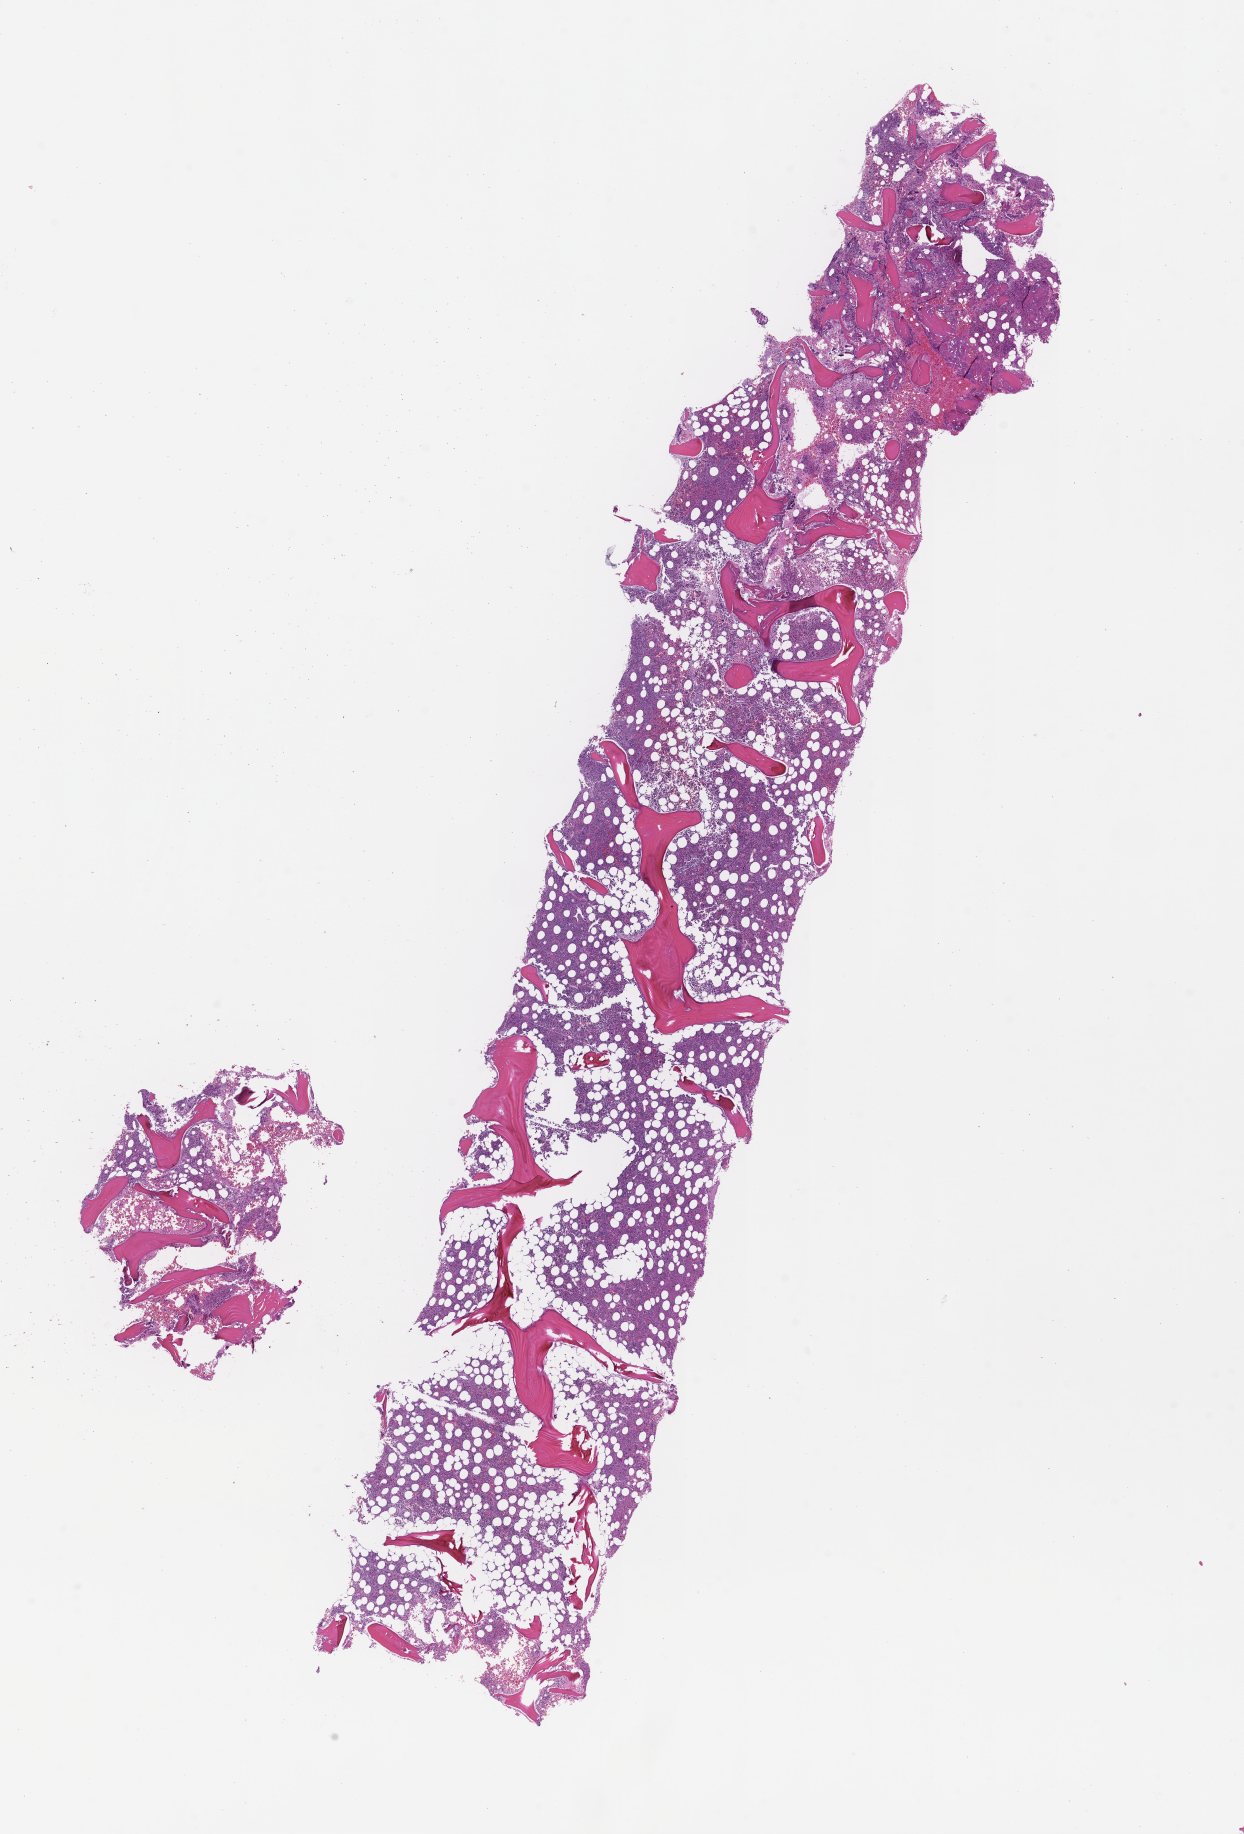
Digitized haematoxylin and eosin-stained section — whole scanned area (about 10.1 x 14.8 mm) shown as a low-resolution overview; formalin-fixed, paraffin-embedded (FFPE) tissue; tissue site: bone marrow; specimen time point: archival tissue. Patient: male.
This section: primary tumour tissue. Diagnosis: Plasma Cell Myeloma.